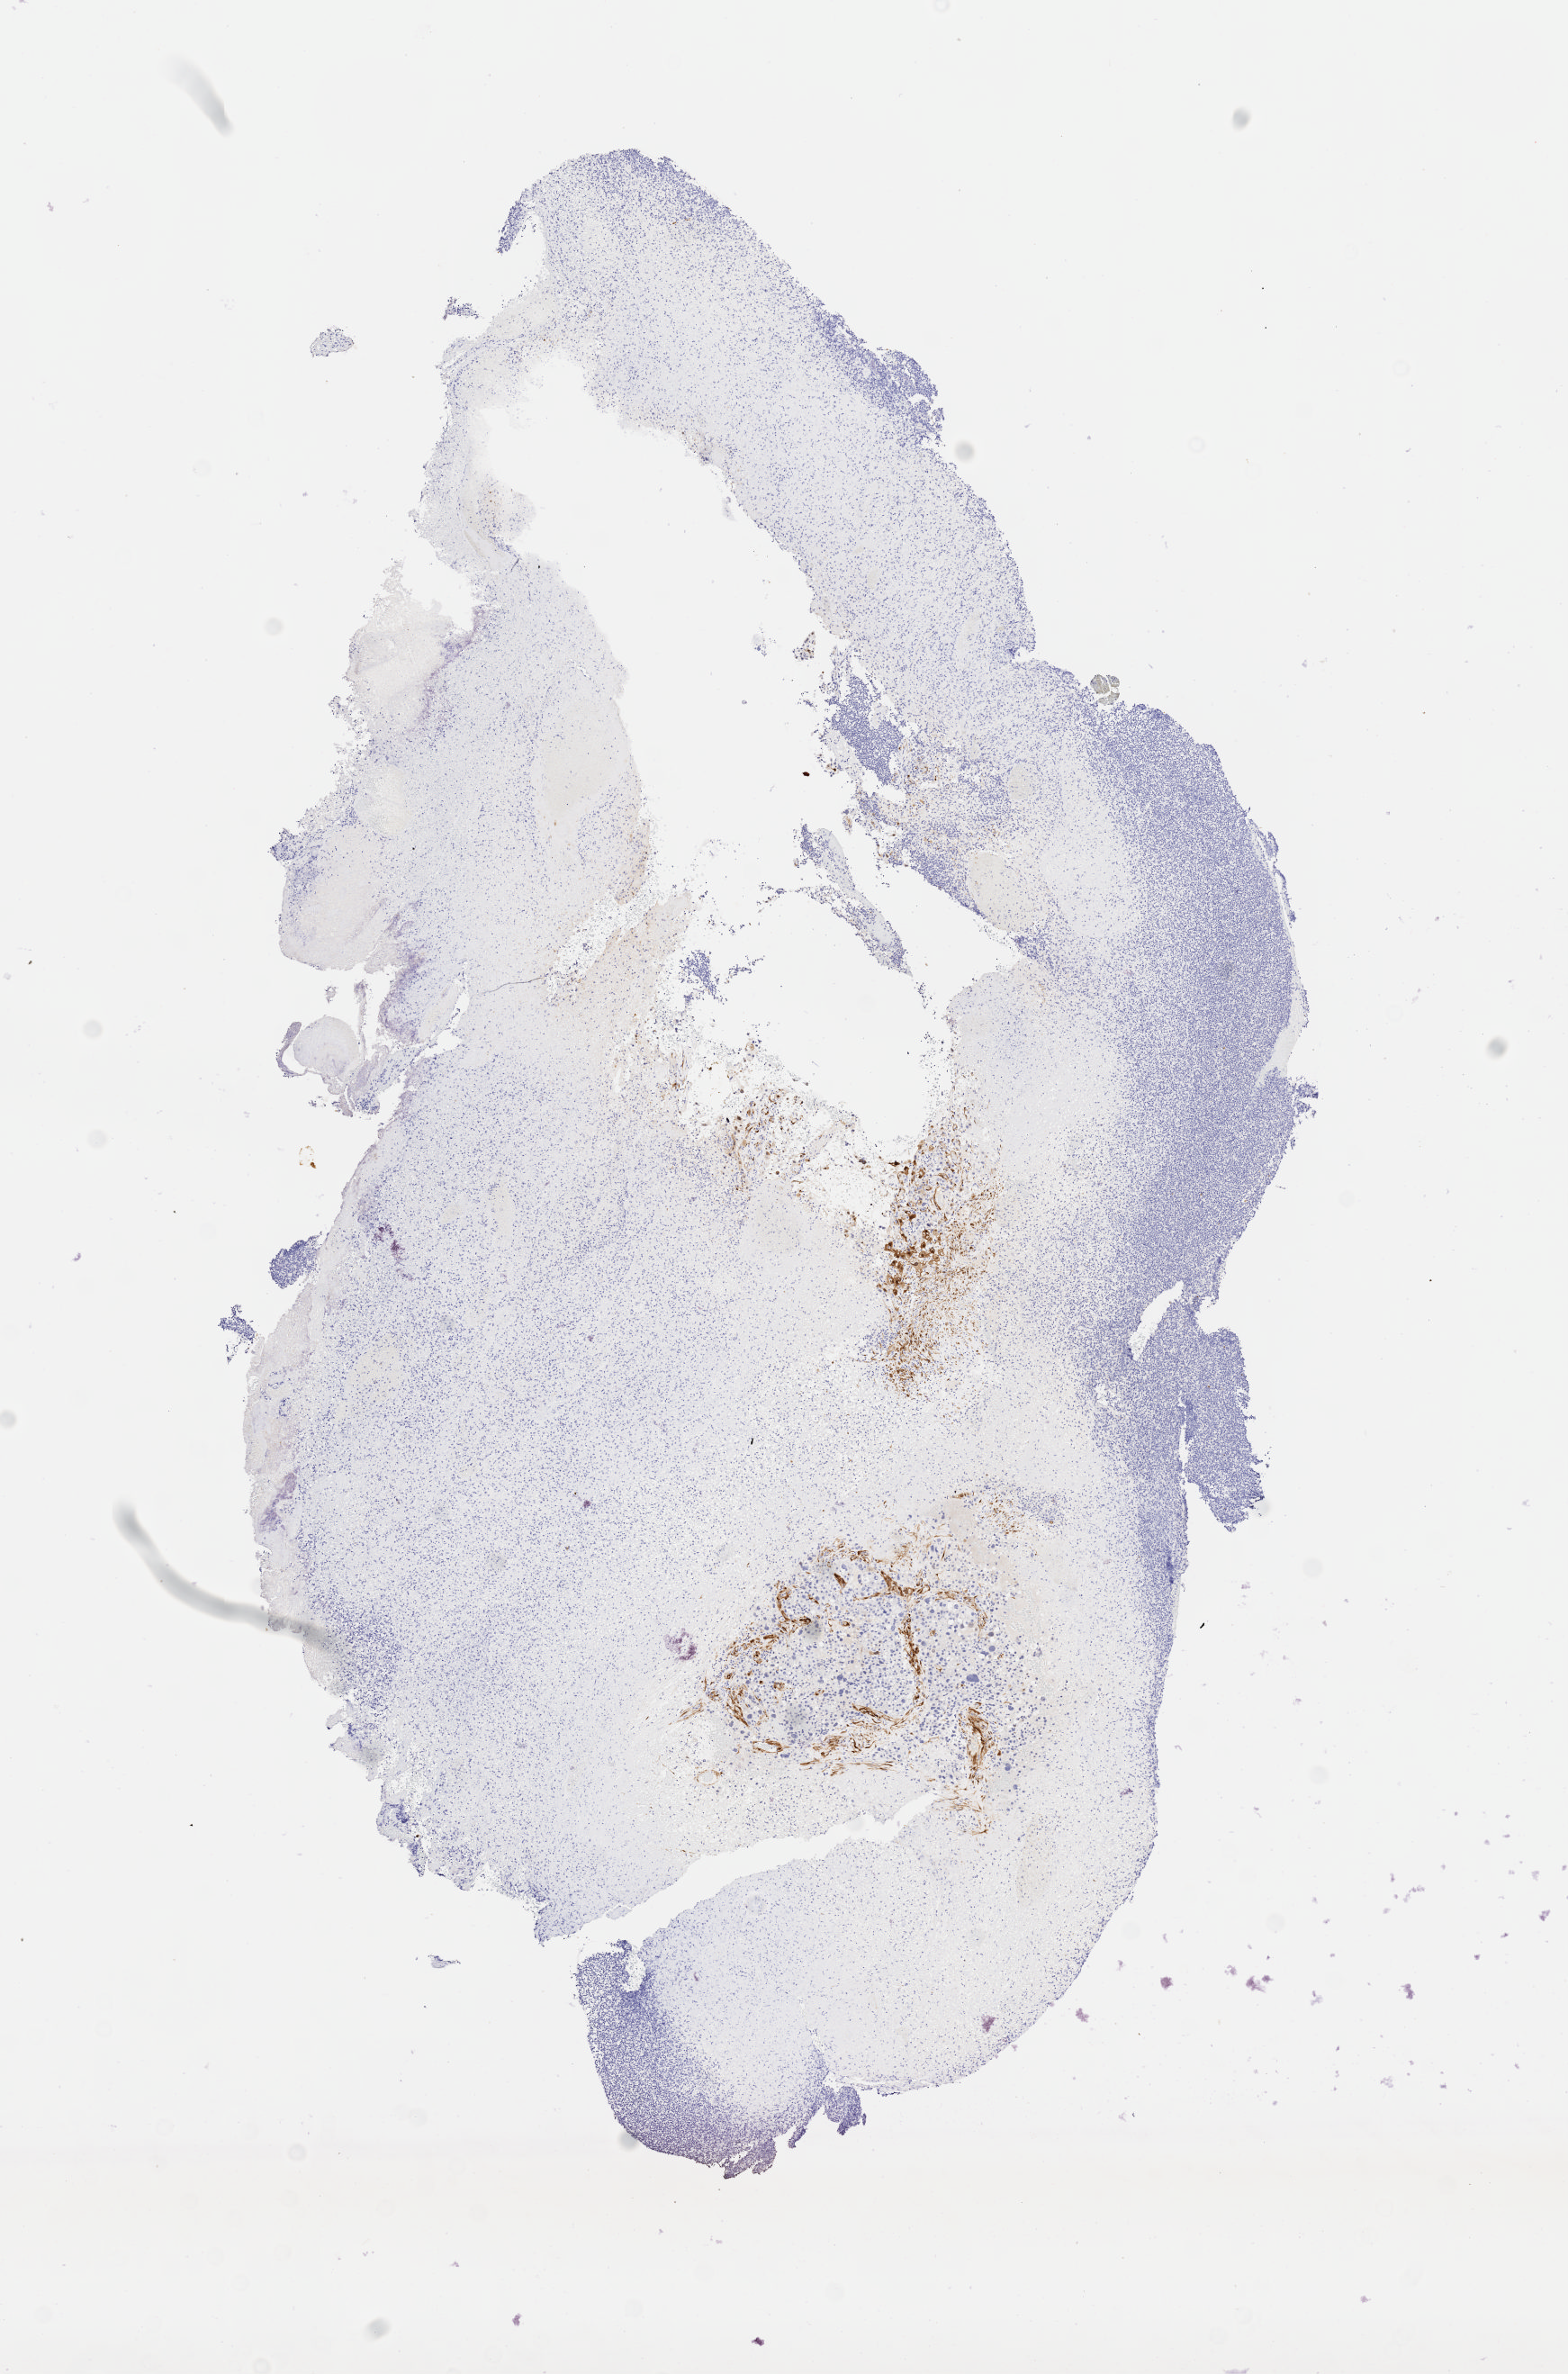
Immunohistochemistry (IHC) whole-slide image stained for p16 (p16INK4a), whole scanned area (about 7.0 x 10.7 mm) shown as a low-resolution overview. Specimen: tumor tissue. Anatomic site: cervix. Patient: female, 62 years old.
Diagnosis: Squamous cell carcinoma, large cell, nonkeratinizing, NOS.